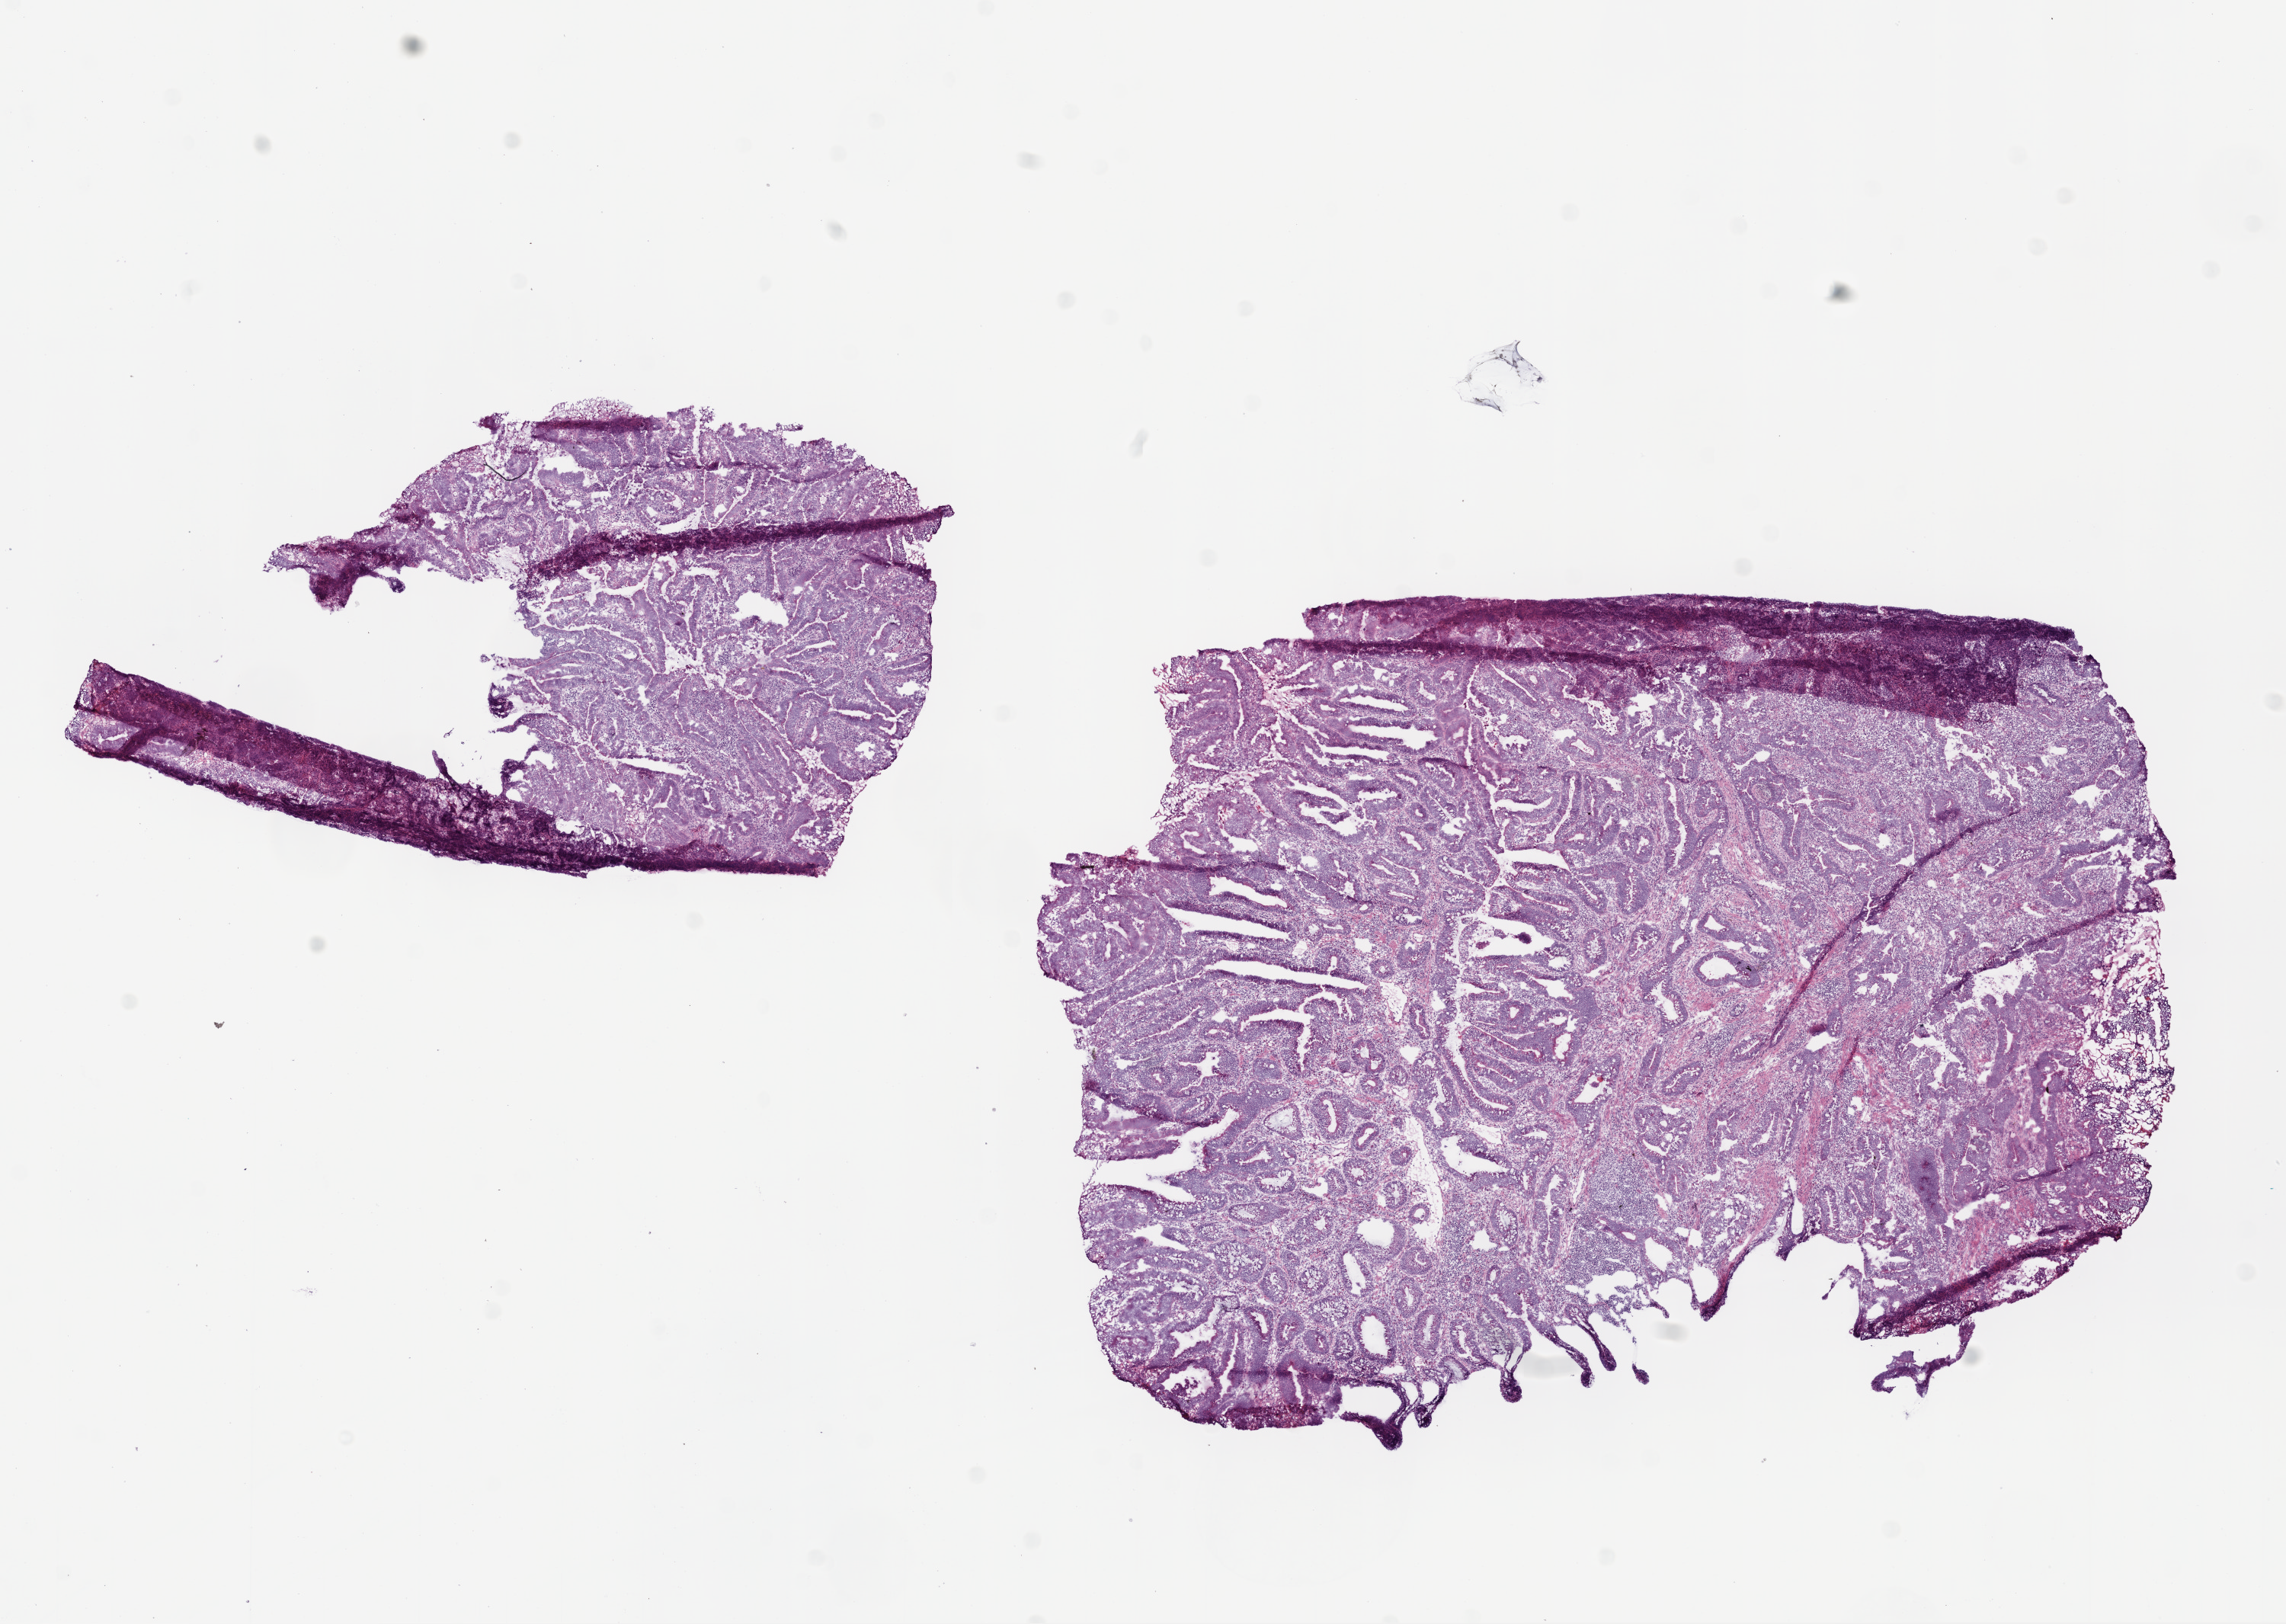
Digitized Hematoxylin and eosin (H&E) stained tissue section (whole slide) — whole scanned area (about 12.0 x 8.5 mm, from a 20x scan) shown as a low-resolution overview, frozen section from the top of the tissue portion, primary tumour sample from the rectum. Patient: male, age at initial diagnosis 62 years. Pathologist review of this section (percent, as recorded): tumour cells 80%, tumour nuclei 75%.
Diagnosis: Adenocarcinoma, NOS.